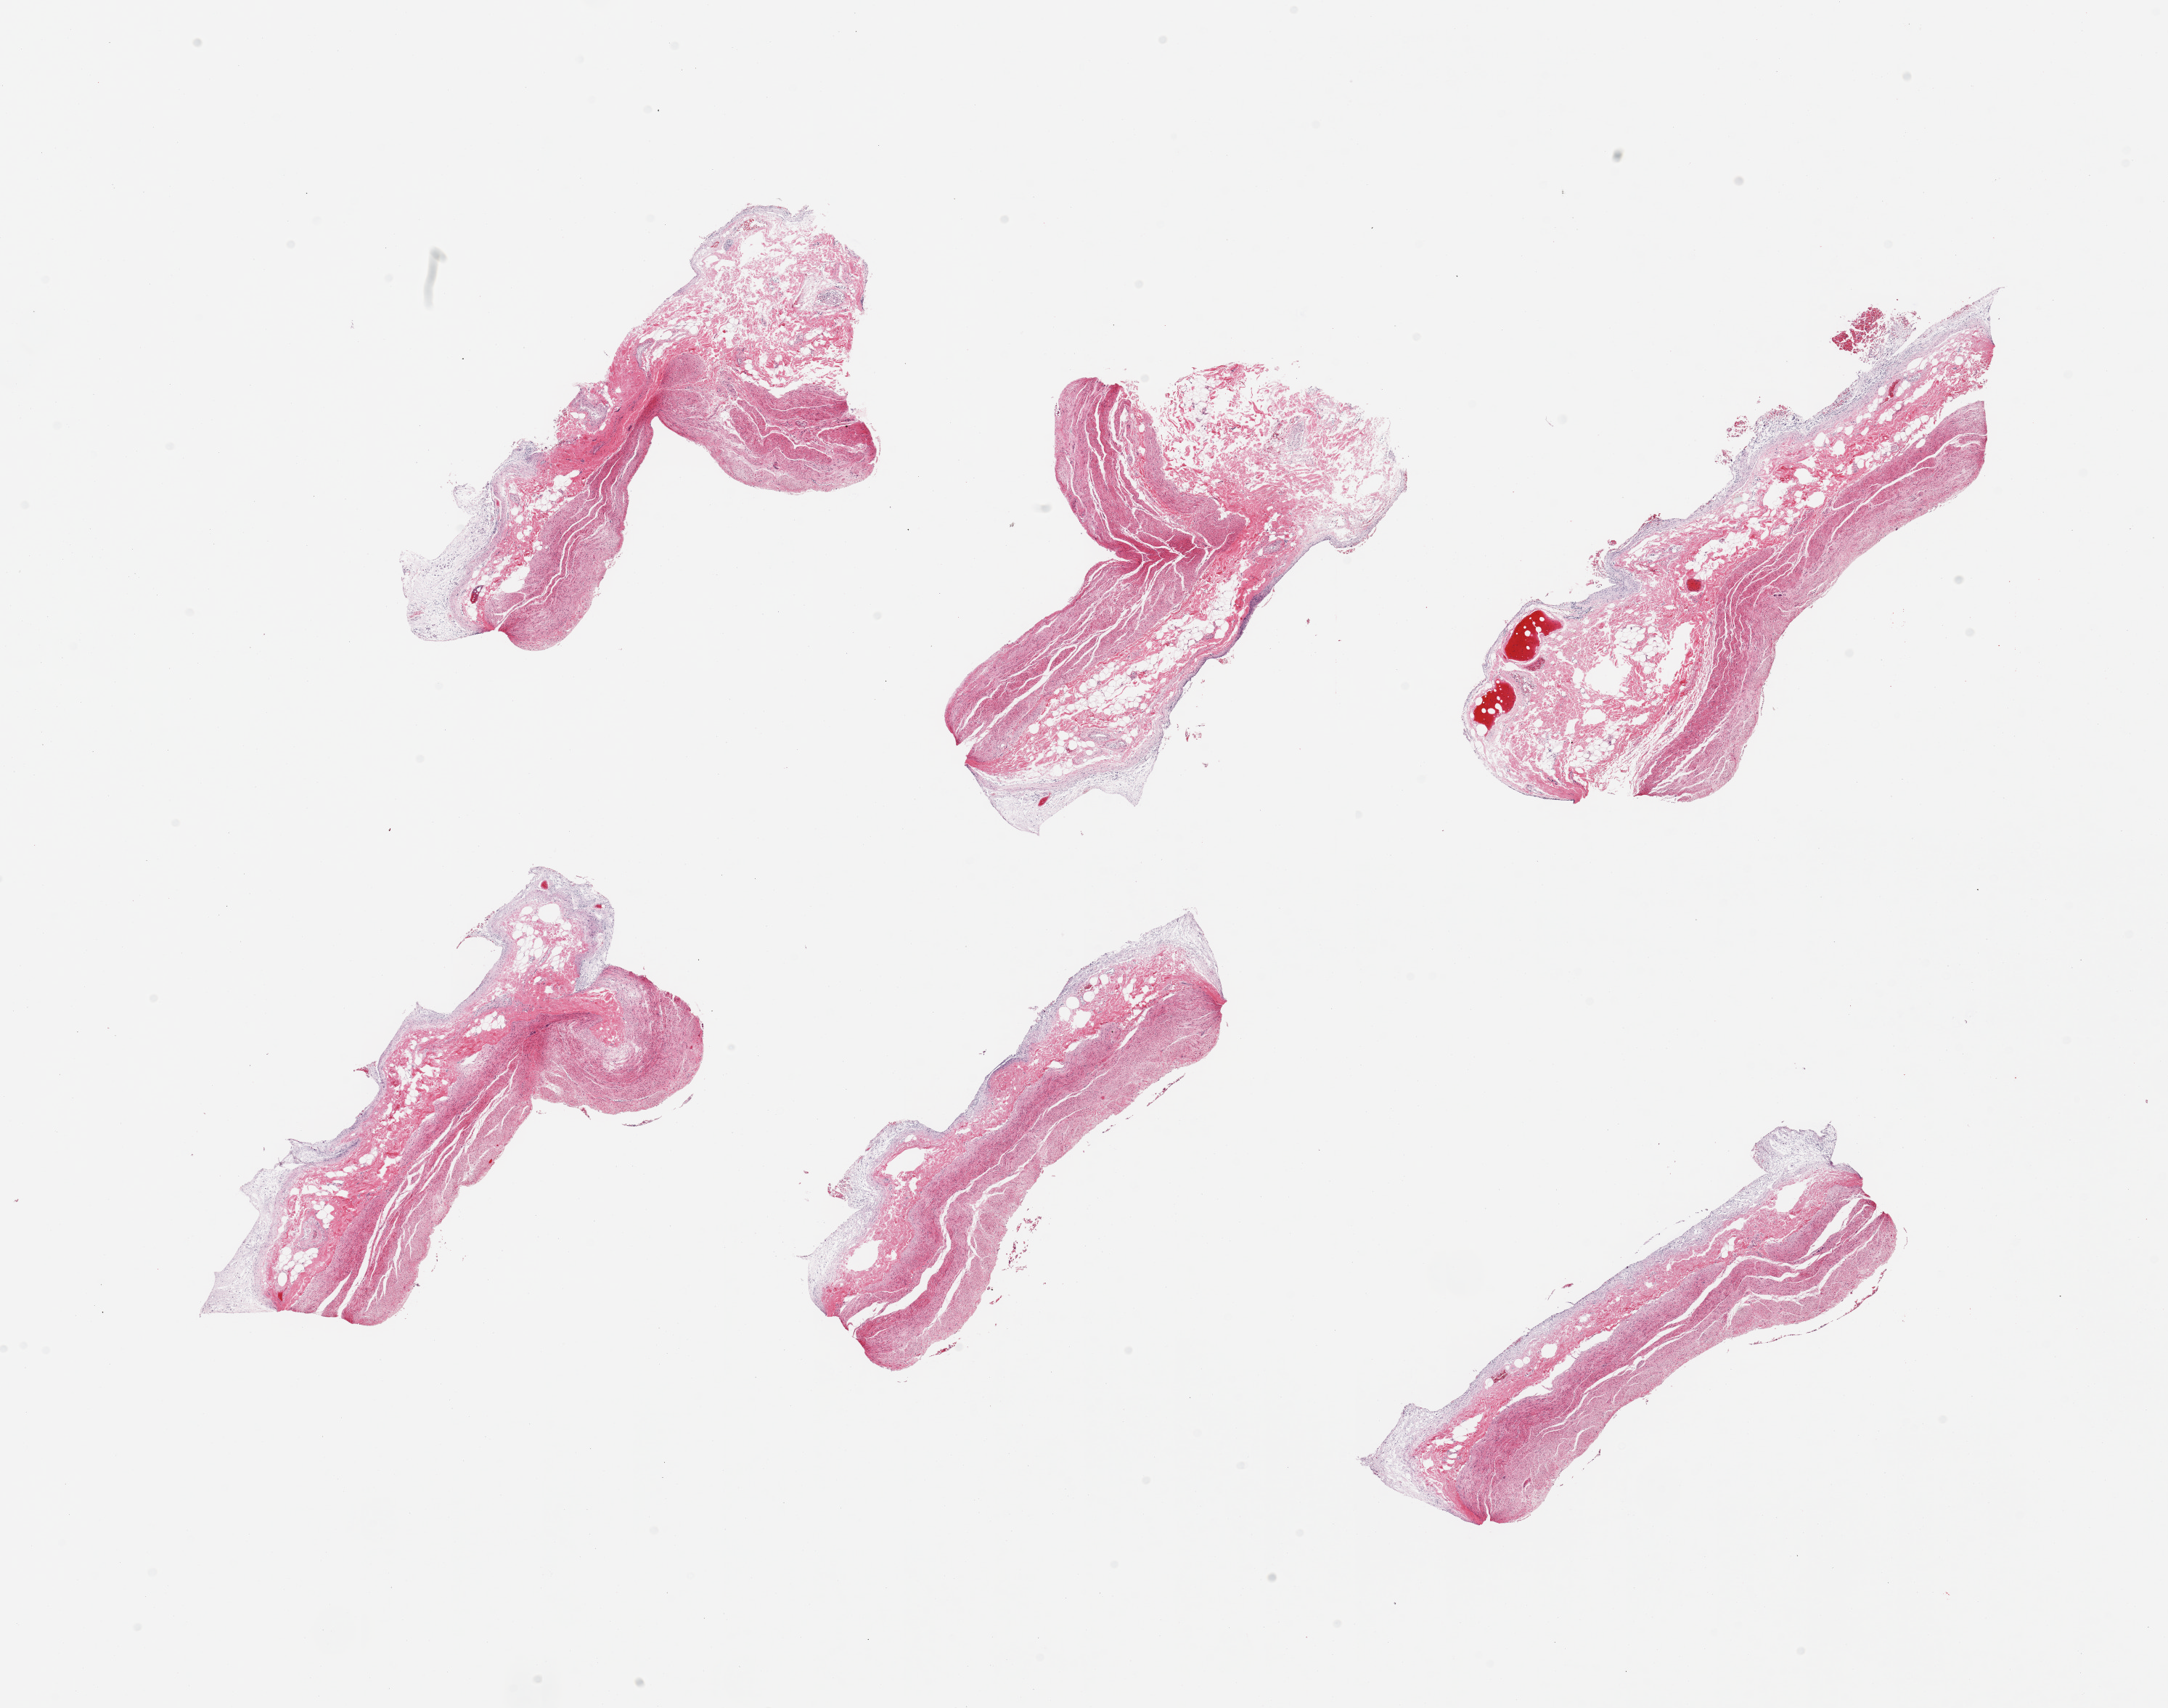
Haematoxylin and eosin whole-slide image — whole scanned area (about 23.6 x 18.6 mm, slide scanned at 20x) shown as a low-resolution overview, PAXgene-fixed, paraffin-embedded tissue, target tissue: stomach, tissue donor sample. Male donor.
* review note (as recorded): 6 pieces; mucosa with advanced autolysis/ghosting; much has sloughed